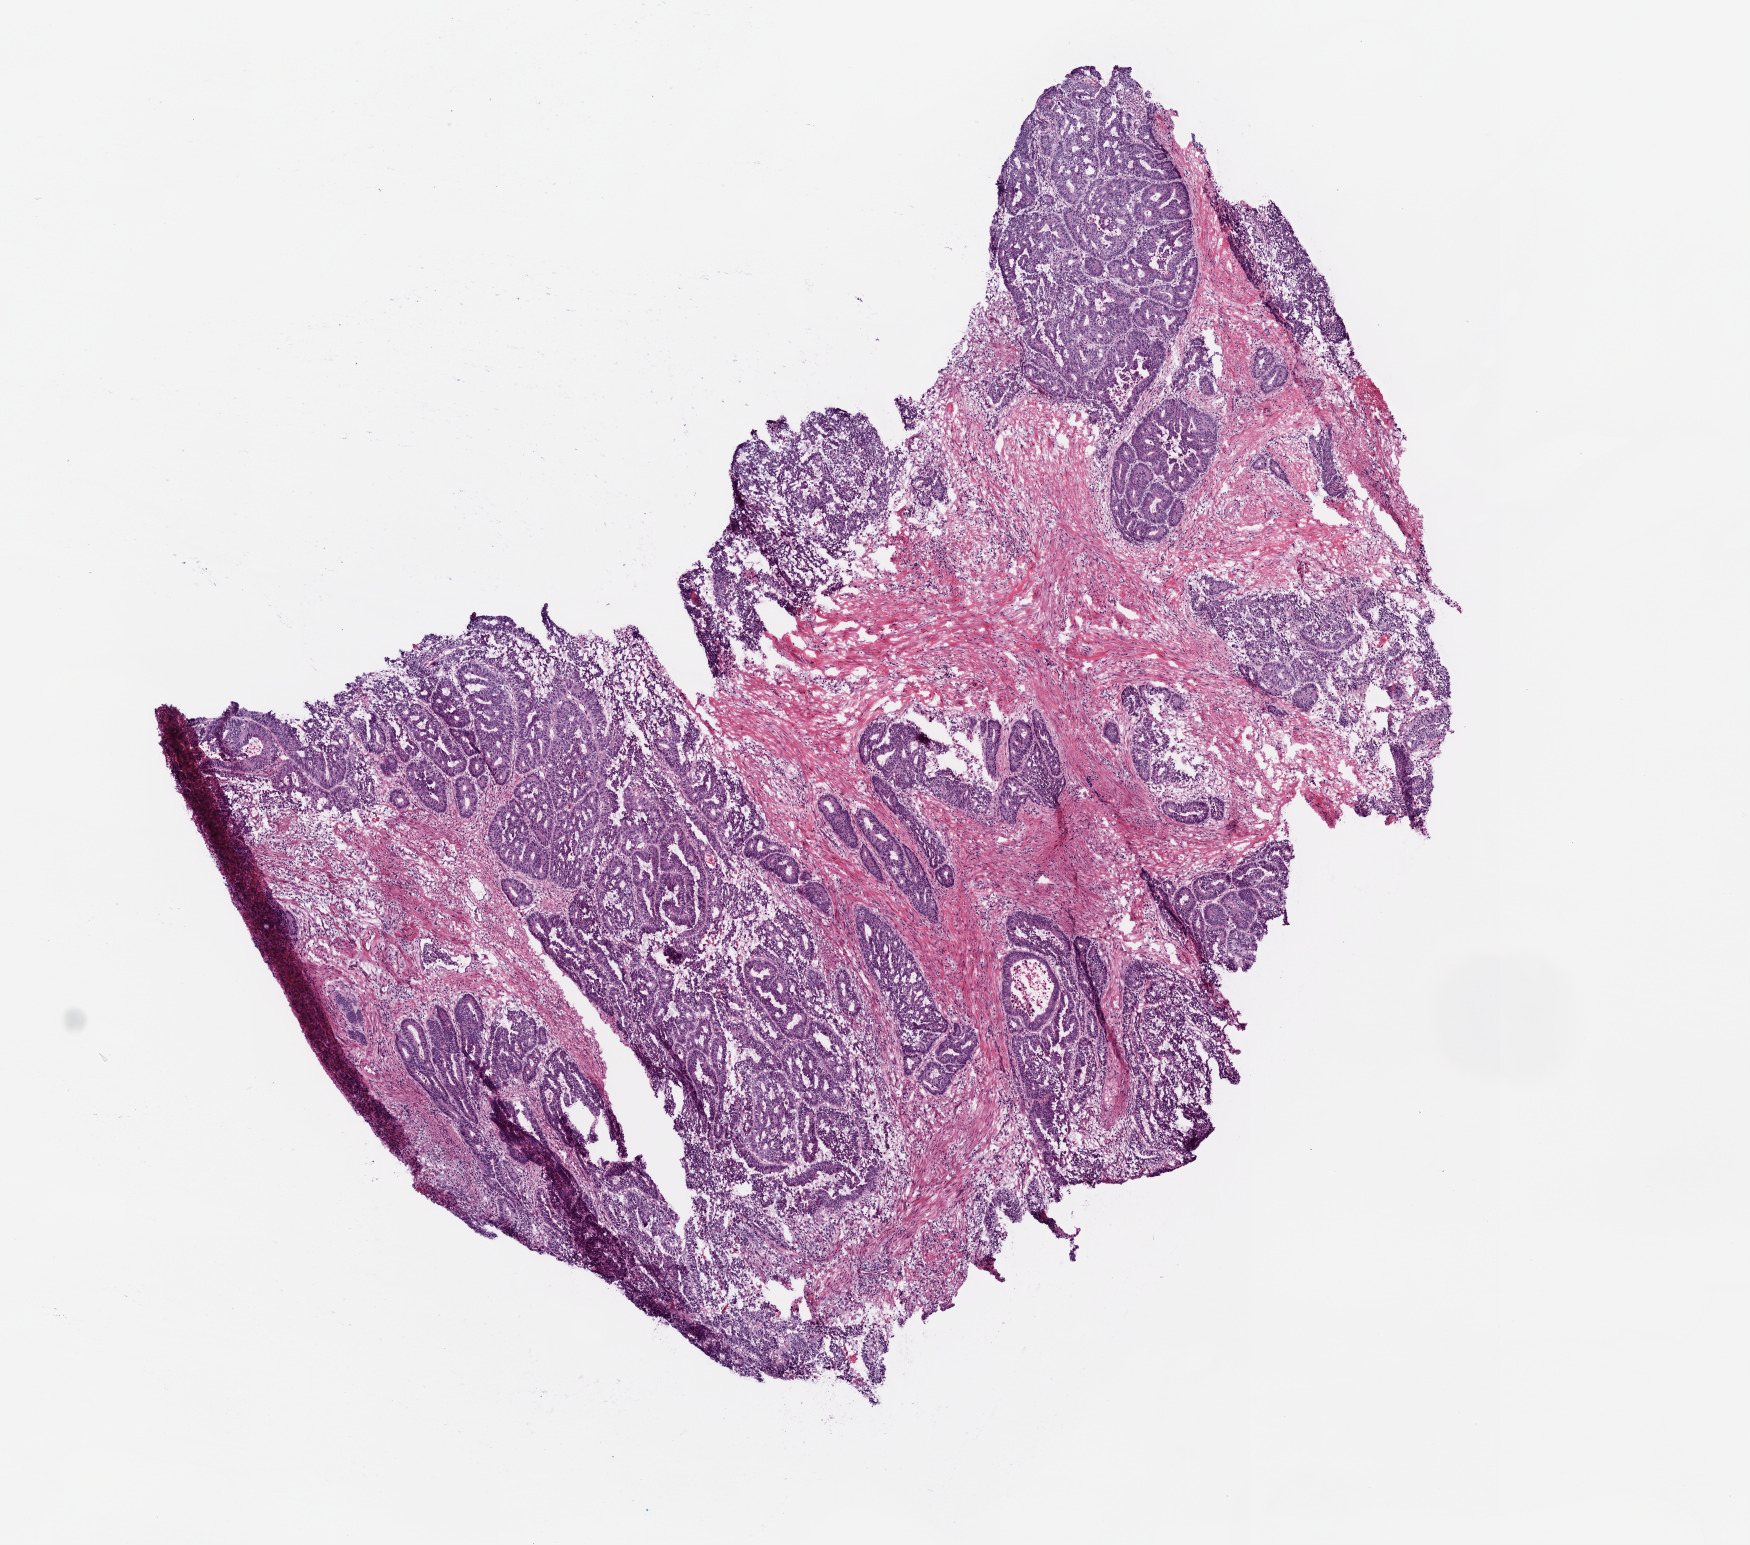
Digitized Hematoxylin and eosin (H&E) stained tissue section (whole slide), shown as a low-resolution overview of the whole scanned area (about 7.0 x 6.2 mm); frozen section from the top of the tissue portion; primary tumour sample from the colon. Female patient; age at initial diagnosis 77 years. Slide review estimates, as recorded: tumour cells 60%, tumour nuclei 75%.
Pathologic diagnosis: Adenocarcinoma, NOS.